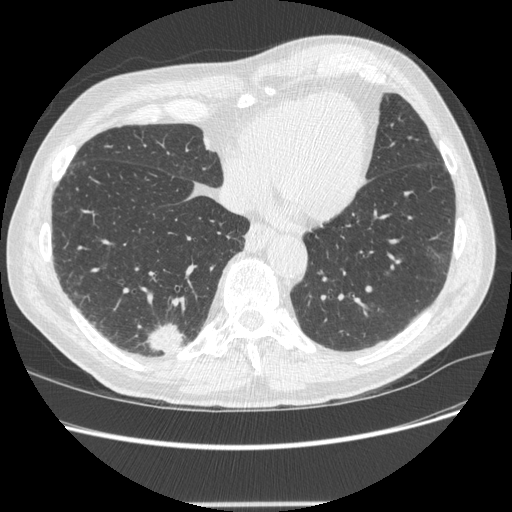
Low-dose screening chest CT, one axial slice; slice 70 of 245 in the series (ordered by position); reconstruction kernel STANDARD; 120 kVp; lung window (W 1500 / L -600 HU); 1.25 mm slice thickness; 512 × 512 image matrix, field of view 372 × 372 mm.
Outlined on this slice (expert manual segmentation):
- lesion 1 (tumor, lower lobe of right lung): bounding box [x1, y1, x2, y2] px = [147, 323, 185, 355]